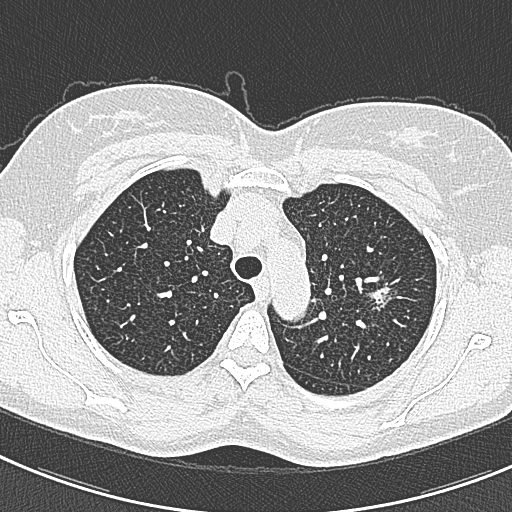
Axial slice from a low-dose chest CT screening exam. Baseline annual screen. Lung window (W 1500 / L -600 HU). 120 kVp. Female participant, aged 57 years at enrolment. Current smoker at enrolment.
Lesion marked by an expert reader, bounding box <362,272,412,322> (left, top, right, bottom; pixels). The screening reader recorded 2 non-calcified nodules or masses ≥4 mm on this exam (right lower lobe, left upper lobe); which of them this box marks is not recorded. Official screen result: positive, change unspecified: nodule(s) >= 4 mm or enlarging nodule(s), mass(es), or other non-specific abnormalities suspicious for lung cancer. Participant outcome: lung cancer diagnosed 198 days after this screen — adenocarcinoma, NOS, left upper lobe, well differentiated (G1), stage IA (AJCC 6th edition), 10 mm at pathology.